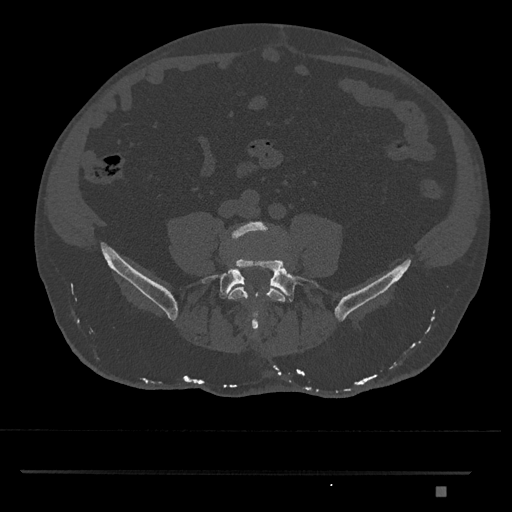
CT including the spine, one axial slice. Slice 578 of 1134 in the series (ordered by position). Reconstruction kernel Br40s/3. 120 kVp. Bone window (W 1800 / L 400 HU). 512 × 512 image matrix, field of view 429 × 429 mm. Patient: male, 65 years. Case-level facts recorded for this patient, not image findings: primary cancer: prostate.
Structures marked on this image (semi-automatic segmentation, software-assisted and operator-edited):
- L4 vertebra: bounding box <228,221,286,322> (left, top, right, bottom; pixels)
- L5 vertebra: <202,258,322,331>